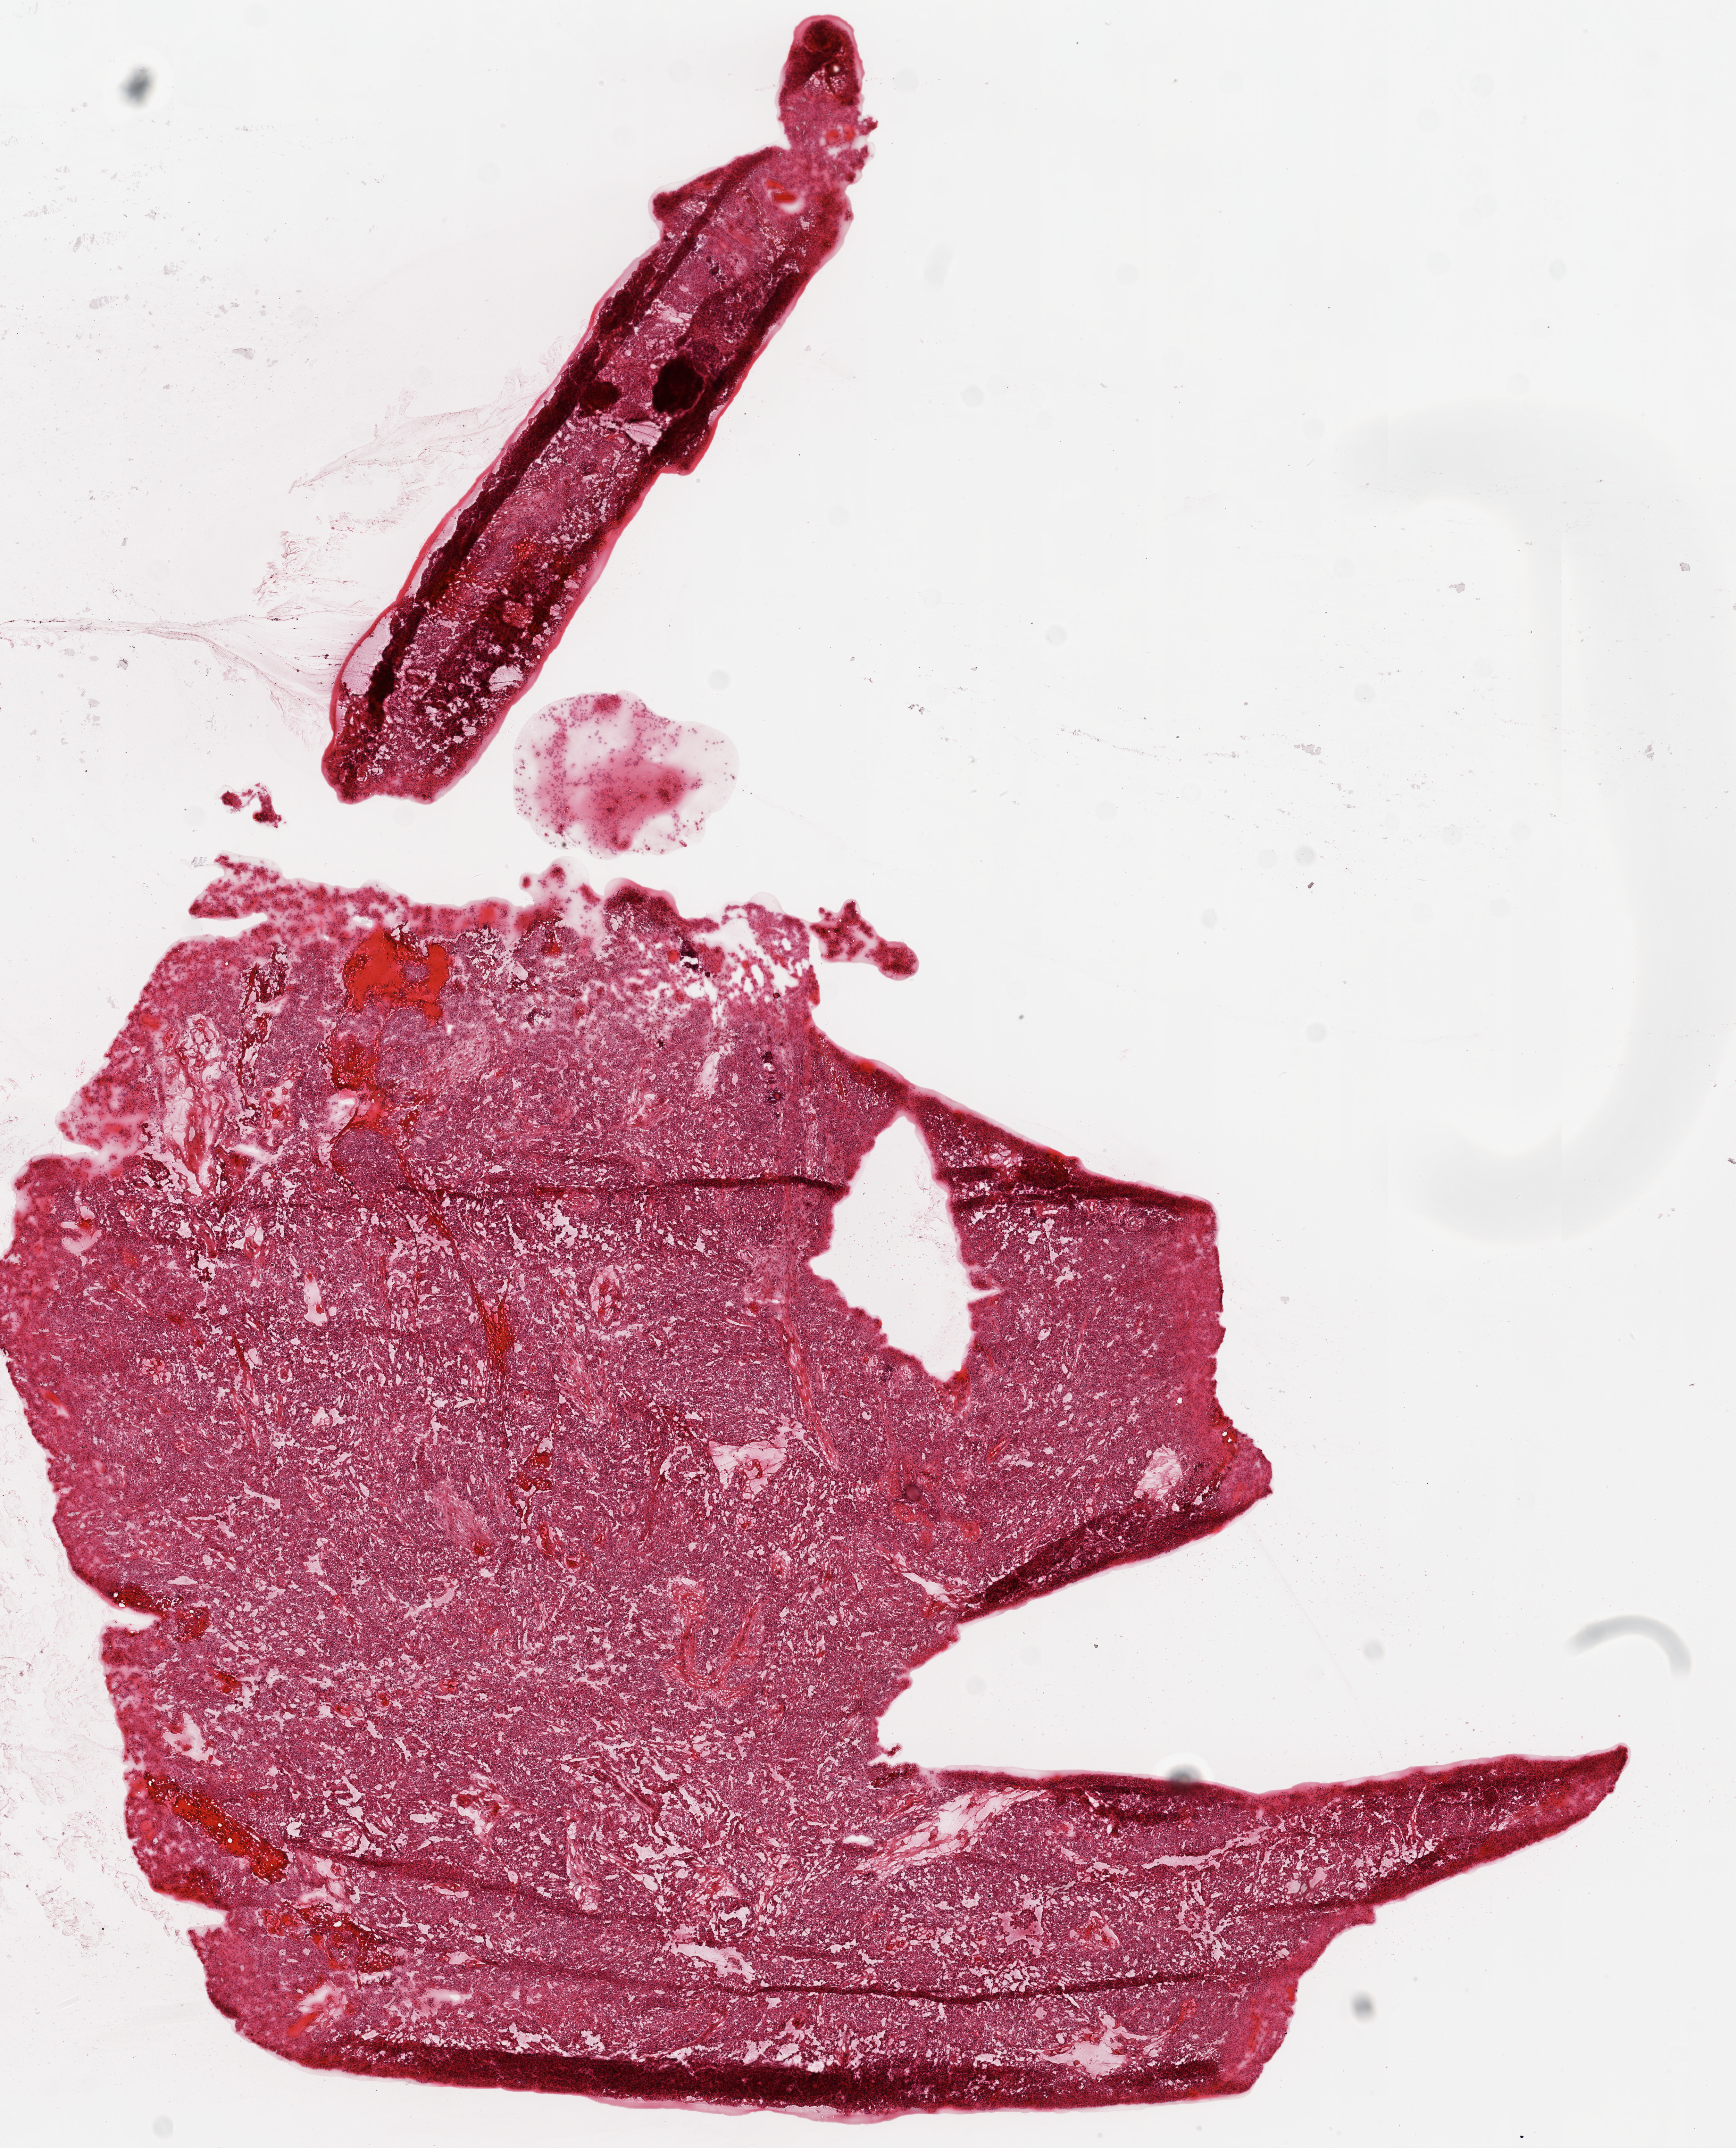
Digitized H&E tissue section (whole slide) — low-resolution overview of the scanned area, about 10.0 x 12.4 mm; frozen section from the top of the tissue portion; ovary, primary tumour sample. Female, age 61 years at initial diagnosis. Histologic grade: G3 (poorly differentiated). Pathologist review of this section (percent, as recorded): tumour cells 85%, tumour nuclei 90%, normal cells 5%, stromal cells 0%, necrosis 10%.
Laterality: bilateral. FIGO stage: IIIC. Diagnosis: Serous cystadenocarcinoma, NOS.